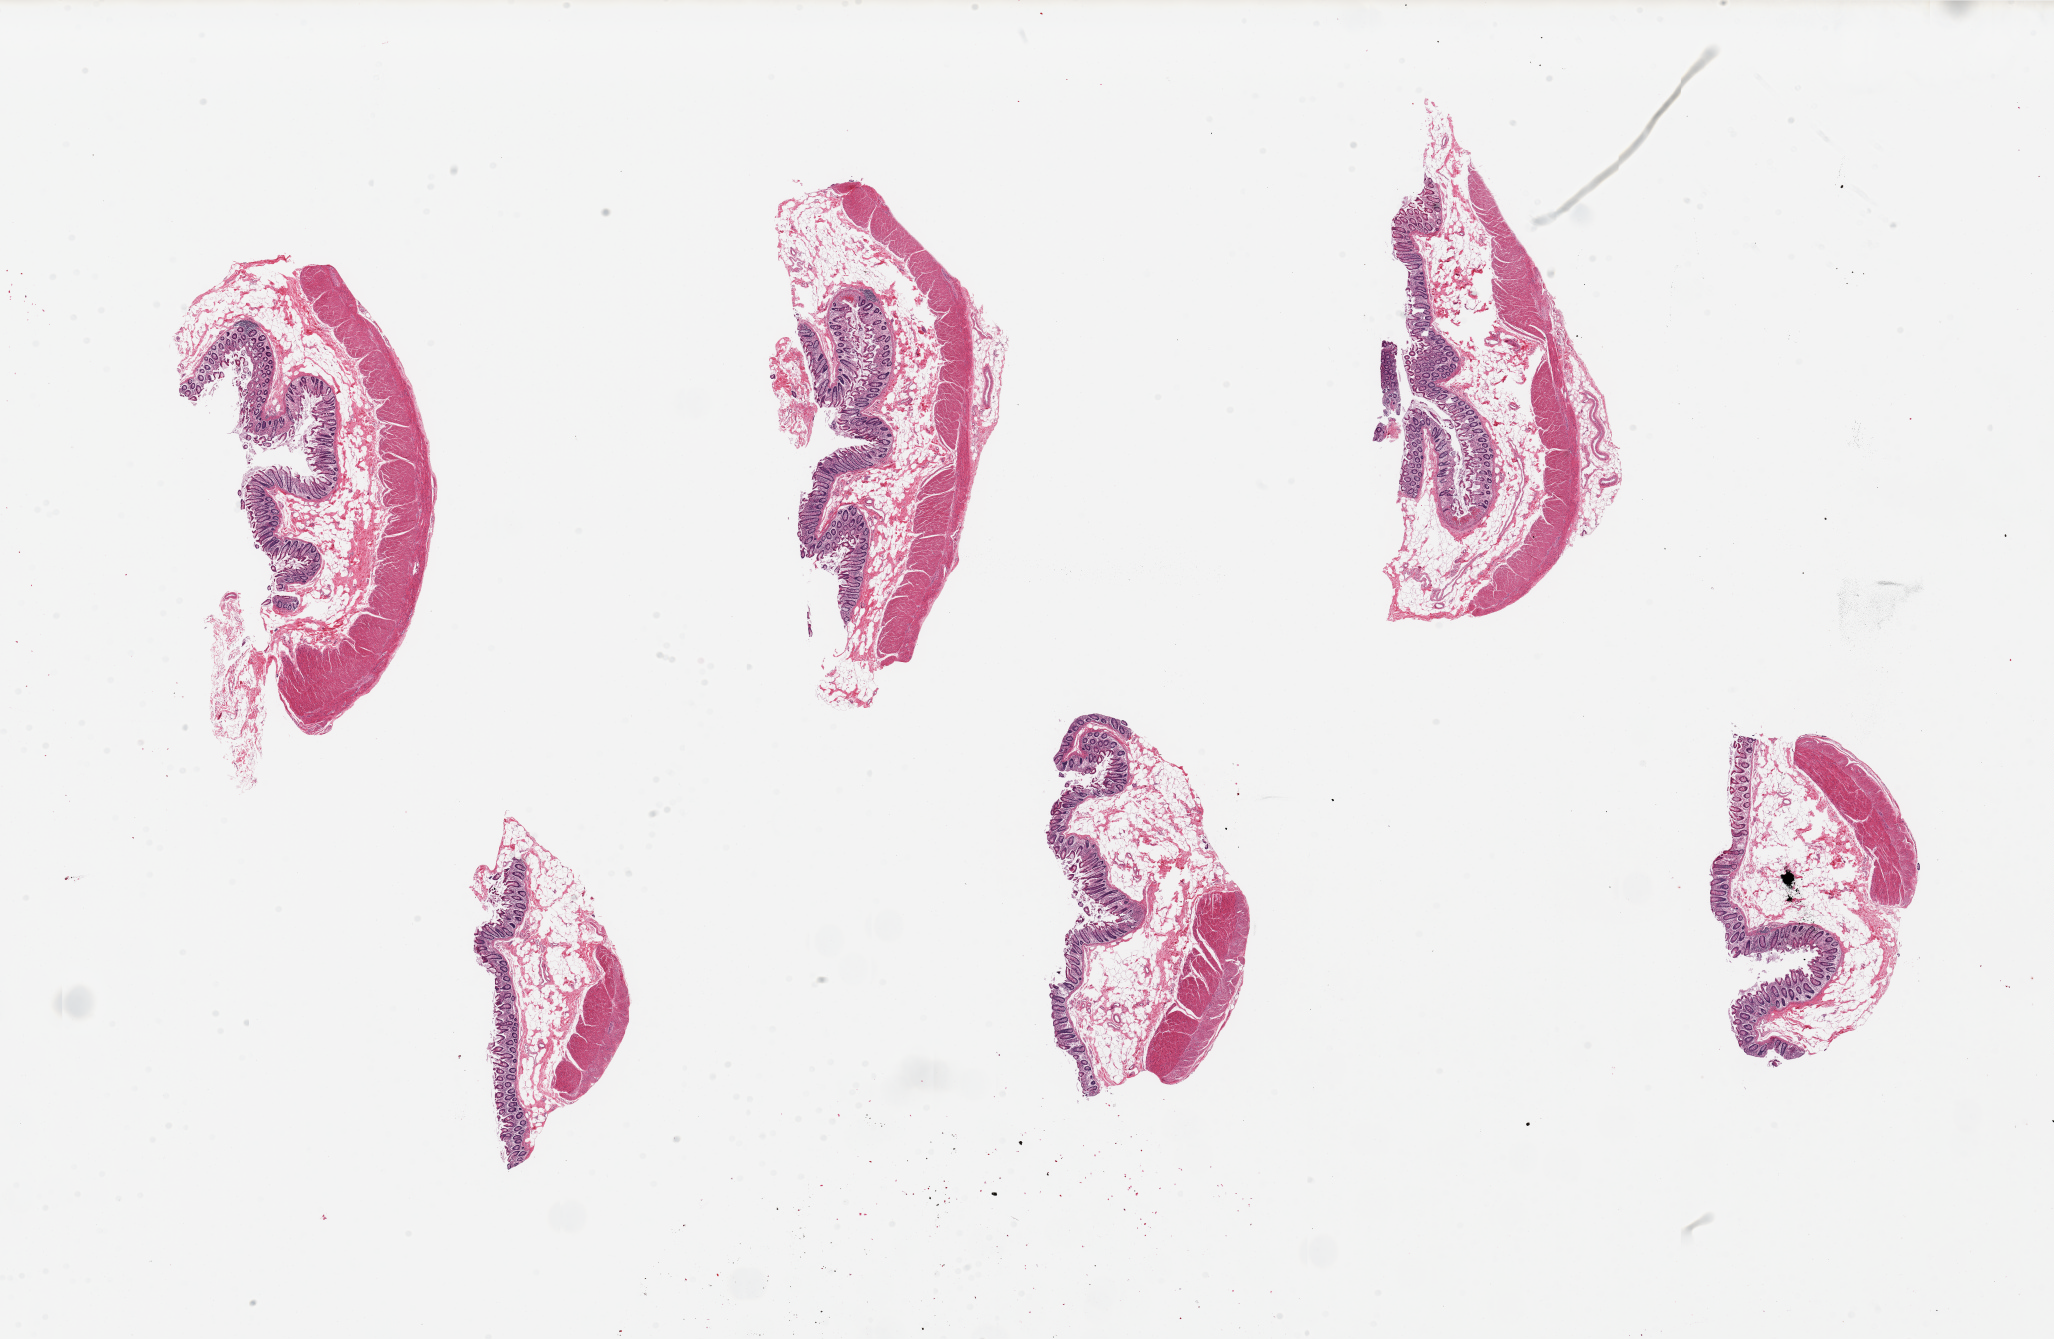
Haematoxylin and eosin whole-slide image, shown as a low-resolution overview of the whole scanned area (about 32.5 x 21.2 mm); PAXgene-fixed, paraffin-embedded tissue; target tissue: transverse colon; donor tissue sample. Male donor.
- reviewer comment on this tissue sample: 6 pieces, up to 8x4mm; mucosa moderately preserved, ~10-20% thickness